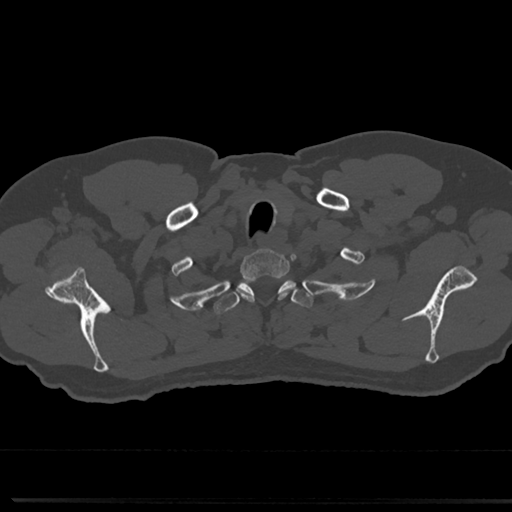
CT including the spine, one axial slice. Position 653 of 817 along the scan axis. Reconstruction kernel Br40s/3. Bone window (W 1800 / L 400 HU). 0.5 mm slice thickness. 512 × 512 image matrix. Male patient, age 61 years. From the clinical record (not read from this slice): primary cancer: prostate.
Annotated regions visible in this slice (semi-automatically segmented with operator editing):
- T1 vertebra: bounding box (x1, y1, x2, y2) in pixels: (240, 250, 288, 276)
- T2 vertebra: (221, 274, 308, 315)